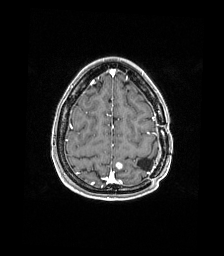
Brain MRI from a brain-tumour surgery series, one axial slice. Slice 44 of 176 in the series (ordered by position). T1-weighted post-contrast. 1 mm slice thickness. 224 × 256 image matrix, field of view 224 × 256 mm. Case-level facts recorded for this patient, not image findings: histopathology: Atypical meningioma; WHO grade: 2; tumour location: Paramedian Left Parietal.
Annotated regions visible in this slice (expert manual segmentation):
- previous resection cavity: box from (x=137, y=158) to (x=153, y=171) px
- tumour: (x=116, y=162)–(x=122, y=169)